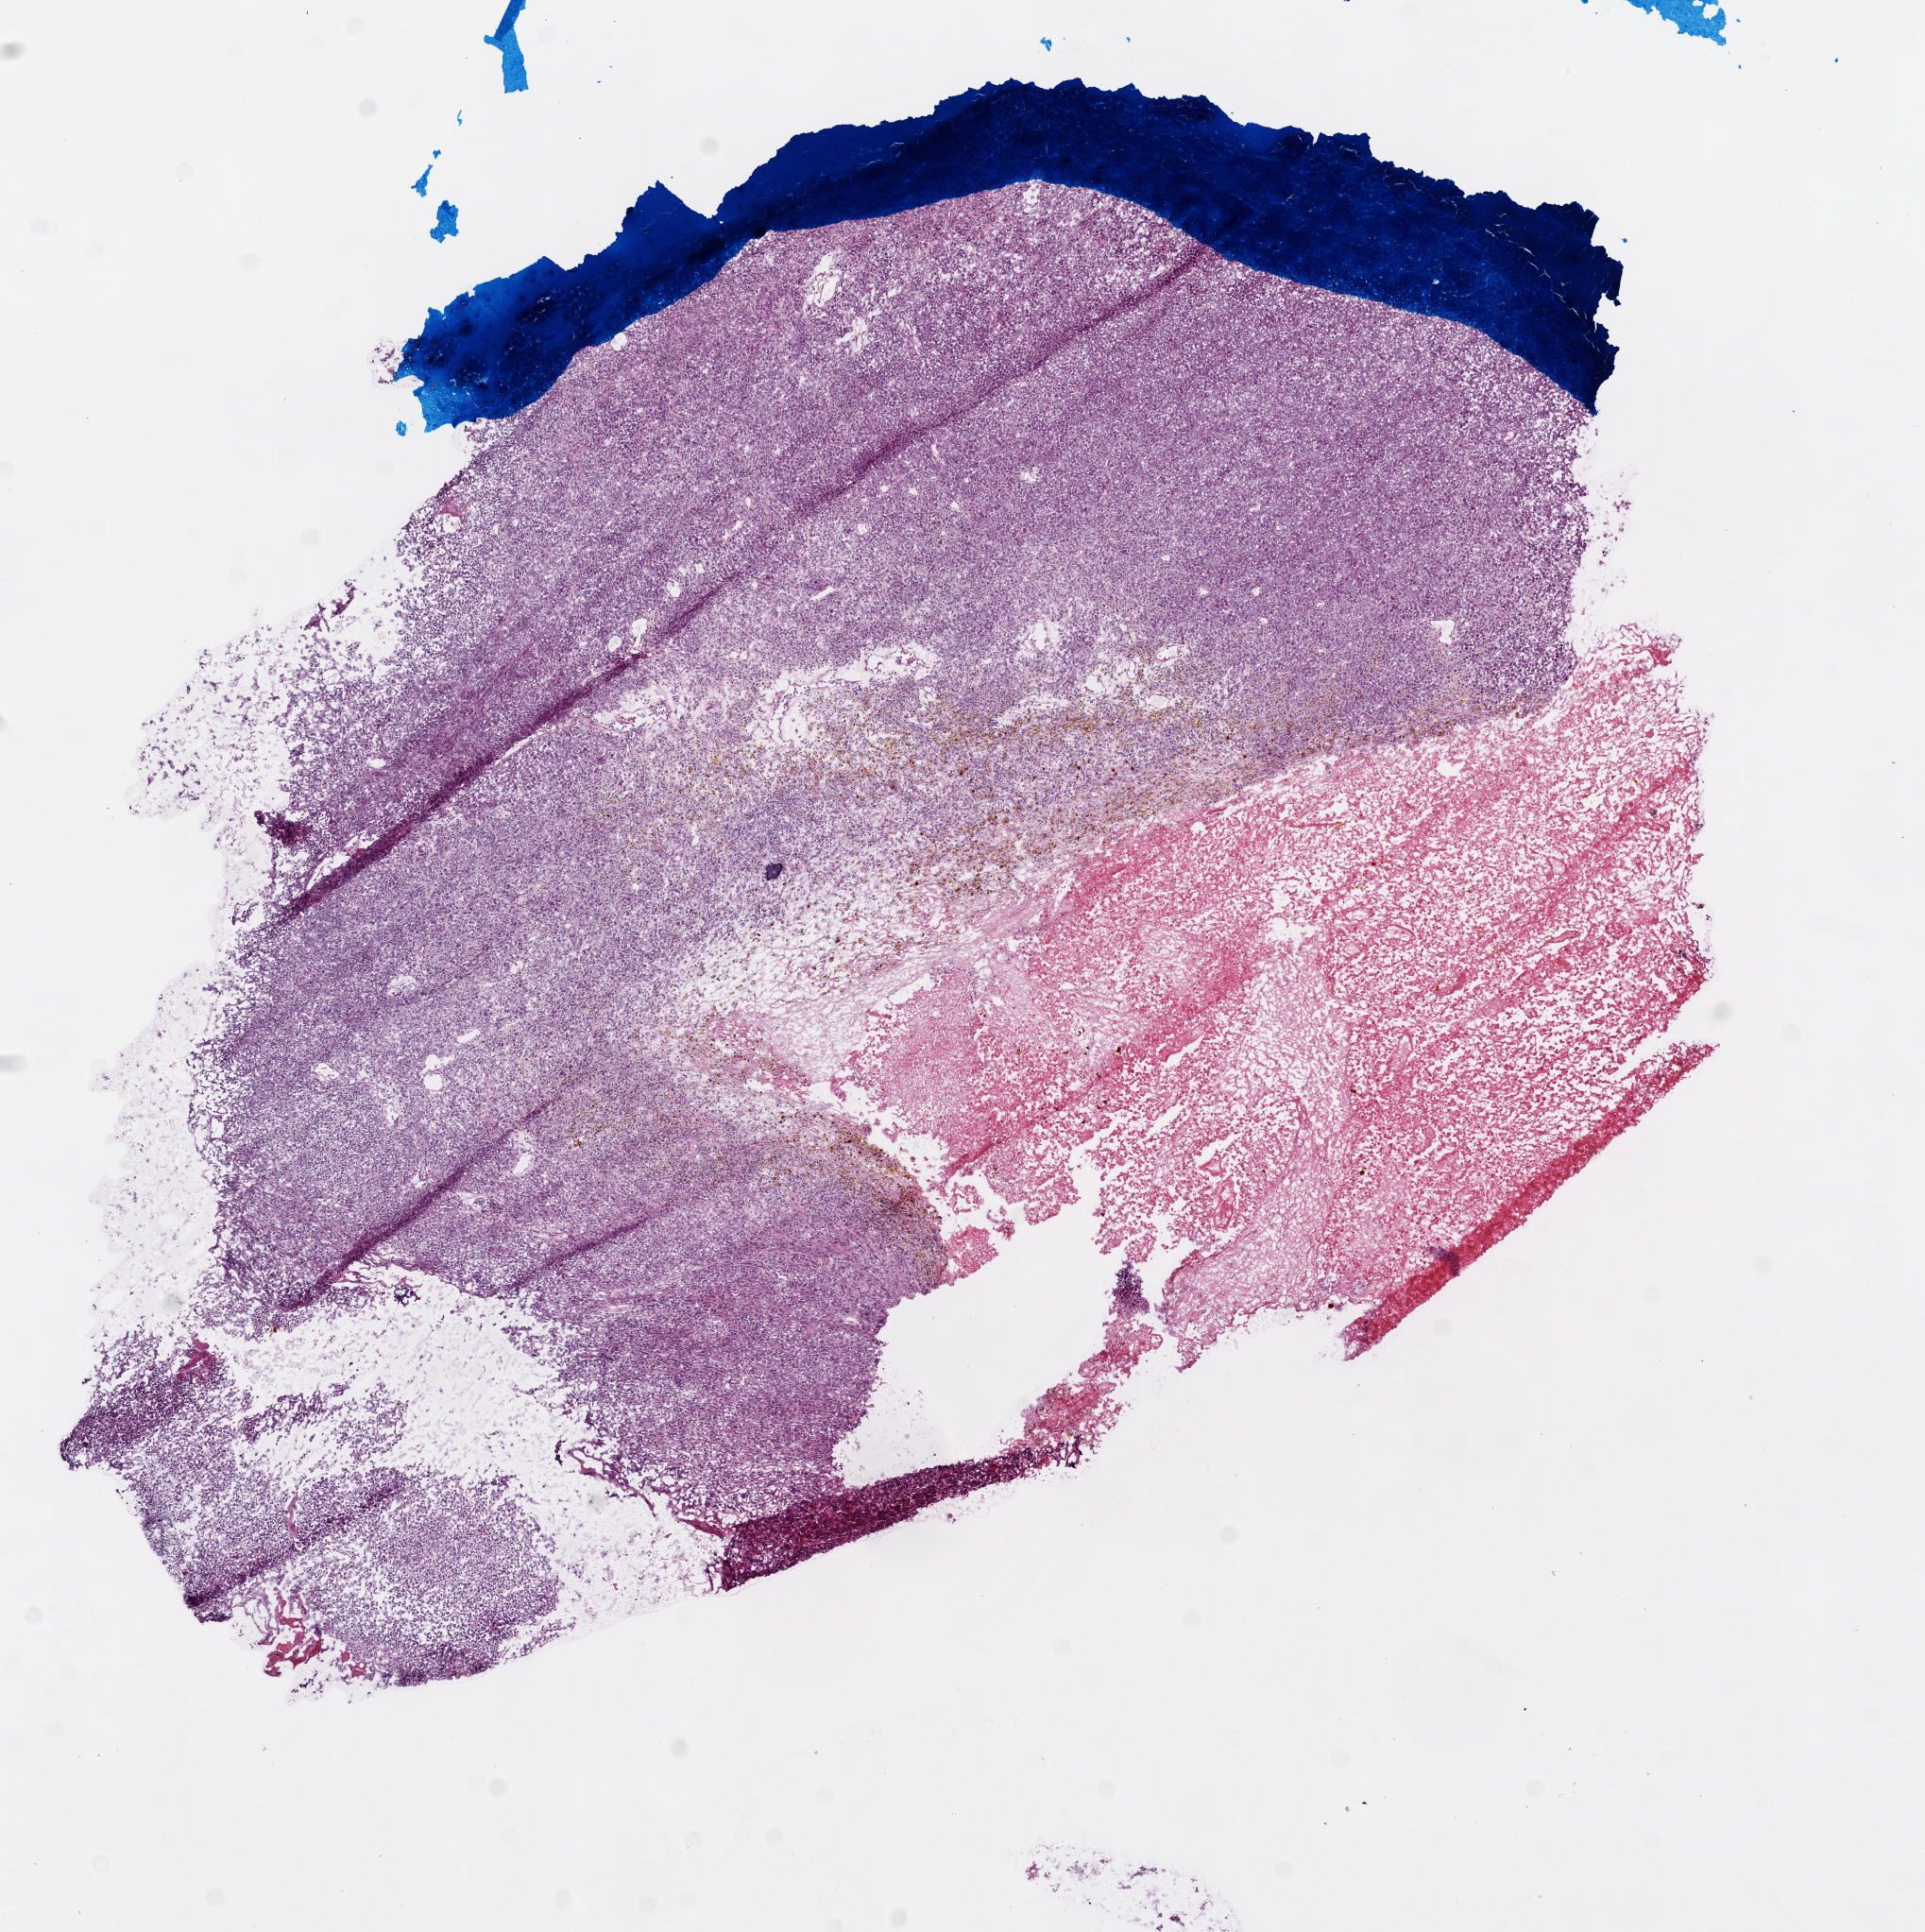
H&E-stained whole-slide image, low-resolution overview of the scanned area, about 8.2 x 8.2 mm, frozen section from the top of the tissue portion, primary tumour sample from the brain. Male, age 61 years at initial diagnosis. Slide review estimates, as recorded: tumour cells 60%, tumour nuclei 90%, normal cells 0%, stromal cells 10%, necrosis 30%.
* histologic diagnosis: Glioblastoma